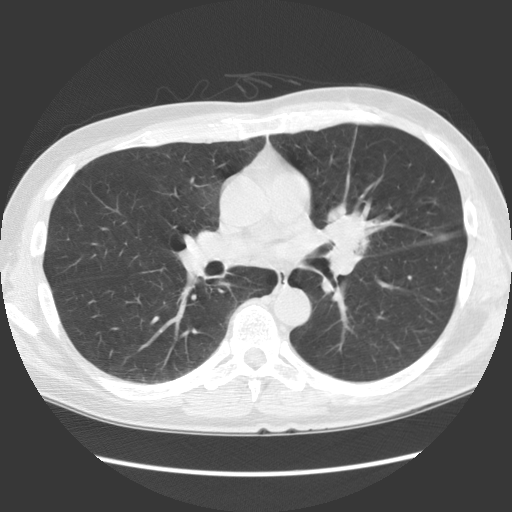
Low-dose screening chest CT, one axial slice; position 72 of 136 along the scan axis; reconstruction kernel STANDARD; 140 kVp; lung window (W 1500 / L -600 HU); 2.5 mm slice thickness; 512 × 512 image matrix.
Outlined on this slice (expert manual segmentation):
- lesion 1 (tumor, hilum of left lung): box from (x=325, y=204) to (x=369, y=254) px